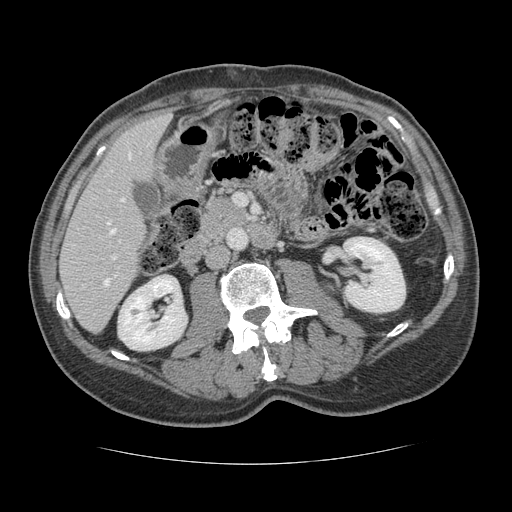
Contrast-enhanced abdominal CT, one axial slice; position 53 of 134 along the scan axis; 120 kVp; intravenous contrast given; soft-tissue window (W 400 / L 40 HU); 2.5 mm slice thickness; 512 × 512 image matrix. Male patient, age 68 years. Case-level facts recorded for this patient, not image findings: diagnosis: colorectal cancer liver metastases, imaged before liver resection; multiple liver metastases: yes.
Structures marked on this image (outlined manually by an expert reader):
- hepatic veins: box from (x=108, y=153) to (x=131, y=233) px
- liver: (x=61, y=115)–(x=169, y=331)
- planned liver remnant (the part of the liver to remain after resection): (x=61, y=115)–(x=169, y=331)
- portal vein (with intrahepatic branches): (x=104, y=256)–(x=116, y=285)